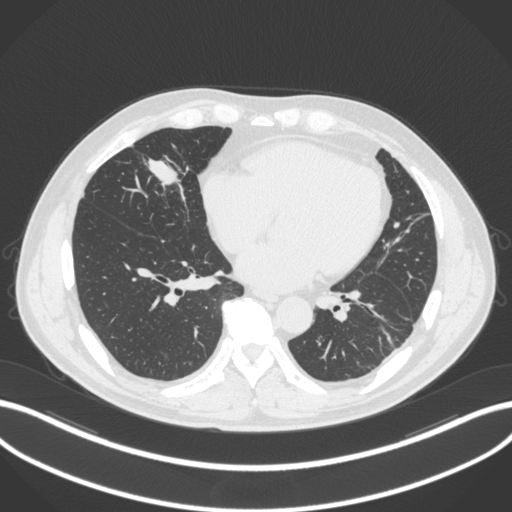
Chest CT, one axial slice. Slice 104 of 399 in the series (ordered by position). Reconstruction kernel B31f. Lung window (W 1500 / L -600 HU). 1 mm slice thickness. 512 × 512 image matrix, field of view 400 × 400 mm. Patient: male, 59 years. From the clinical record (not read from this slice): clinical TNM (as recorded): T2a N1 M0.
Annotated regions visible in this slice (bounding box drawn by a radiologist):
- lung tumour (recorded histology: adenocarcinoma): bounding box (x1, y1, x2, y2) in pixels: (140, 149, 189, 196)